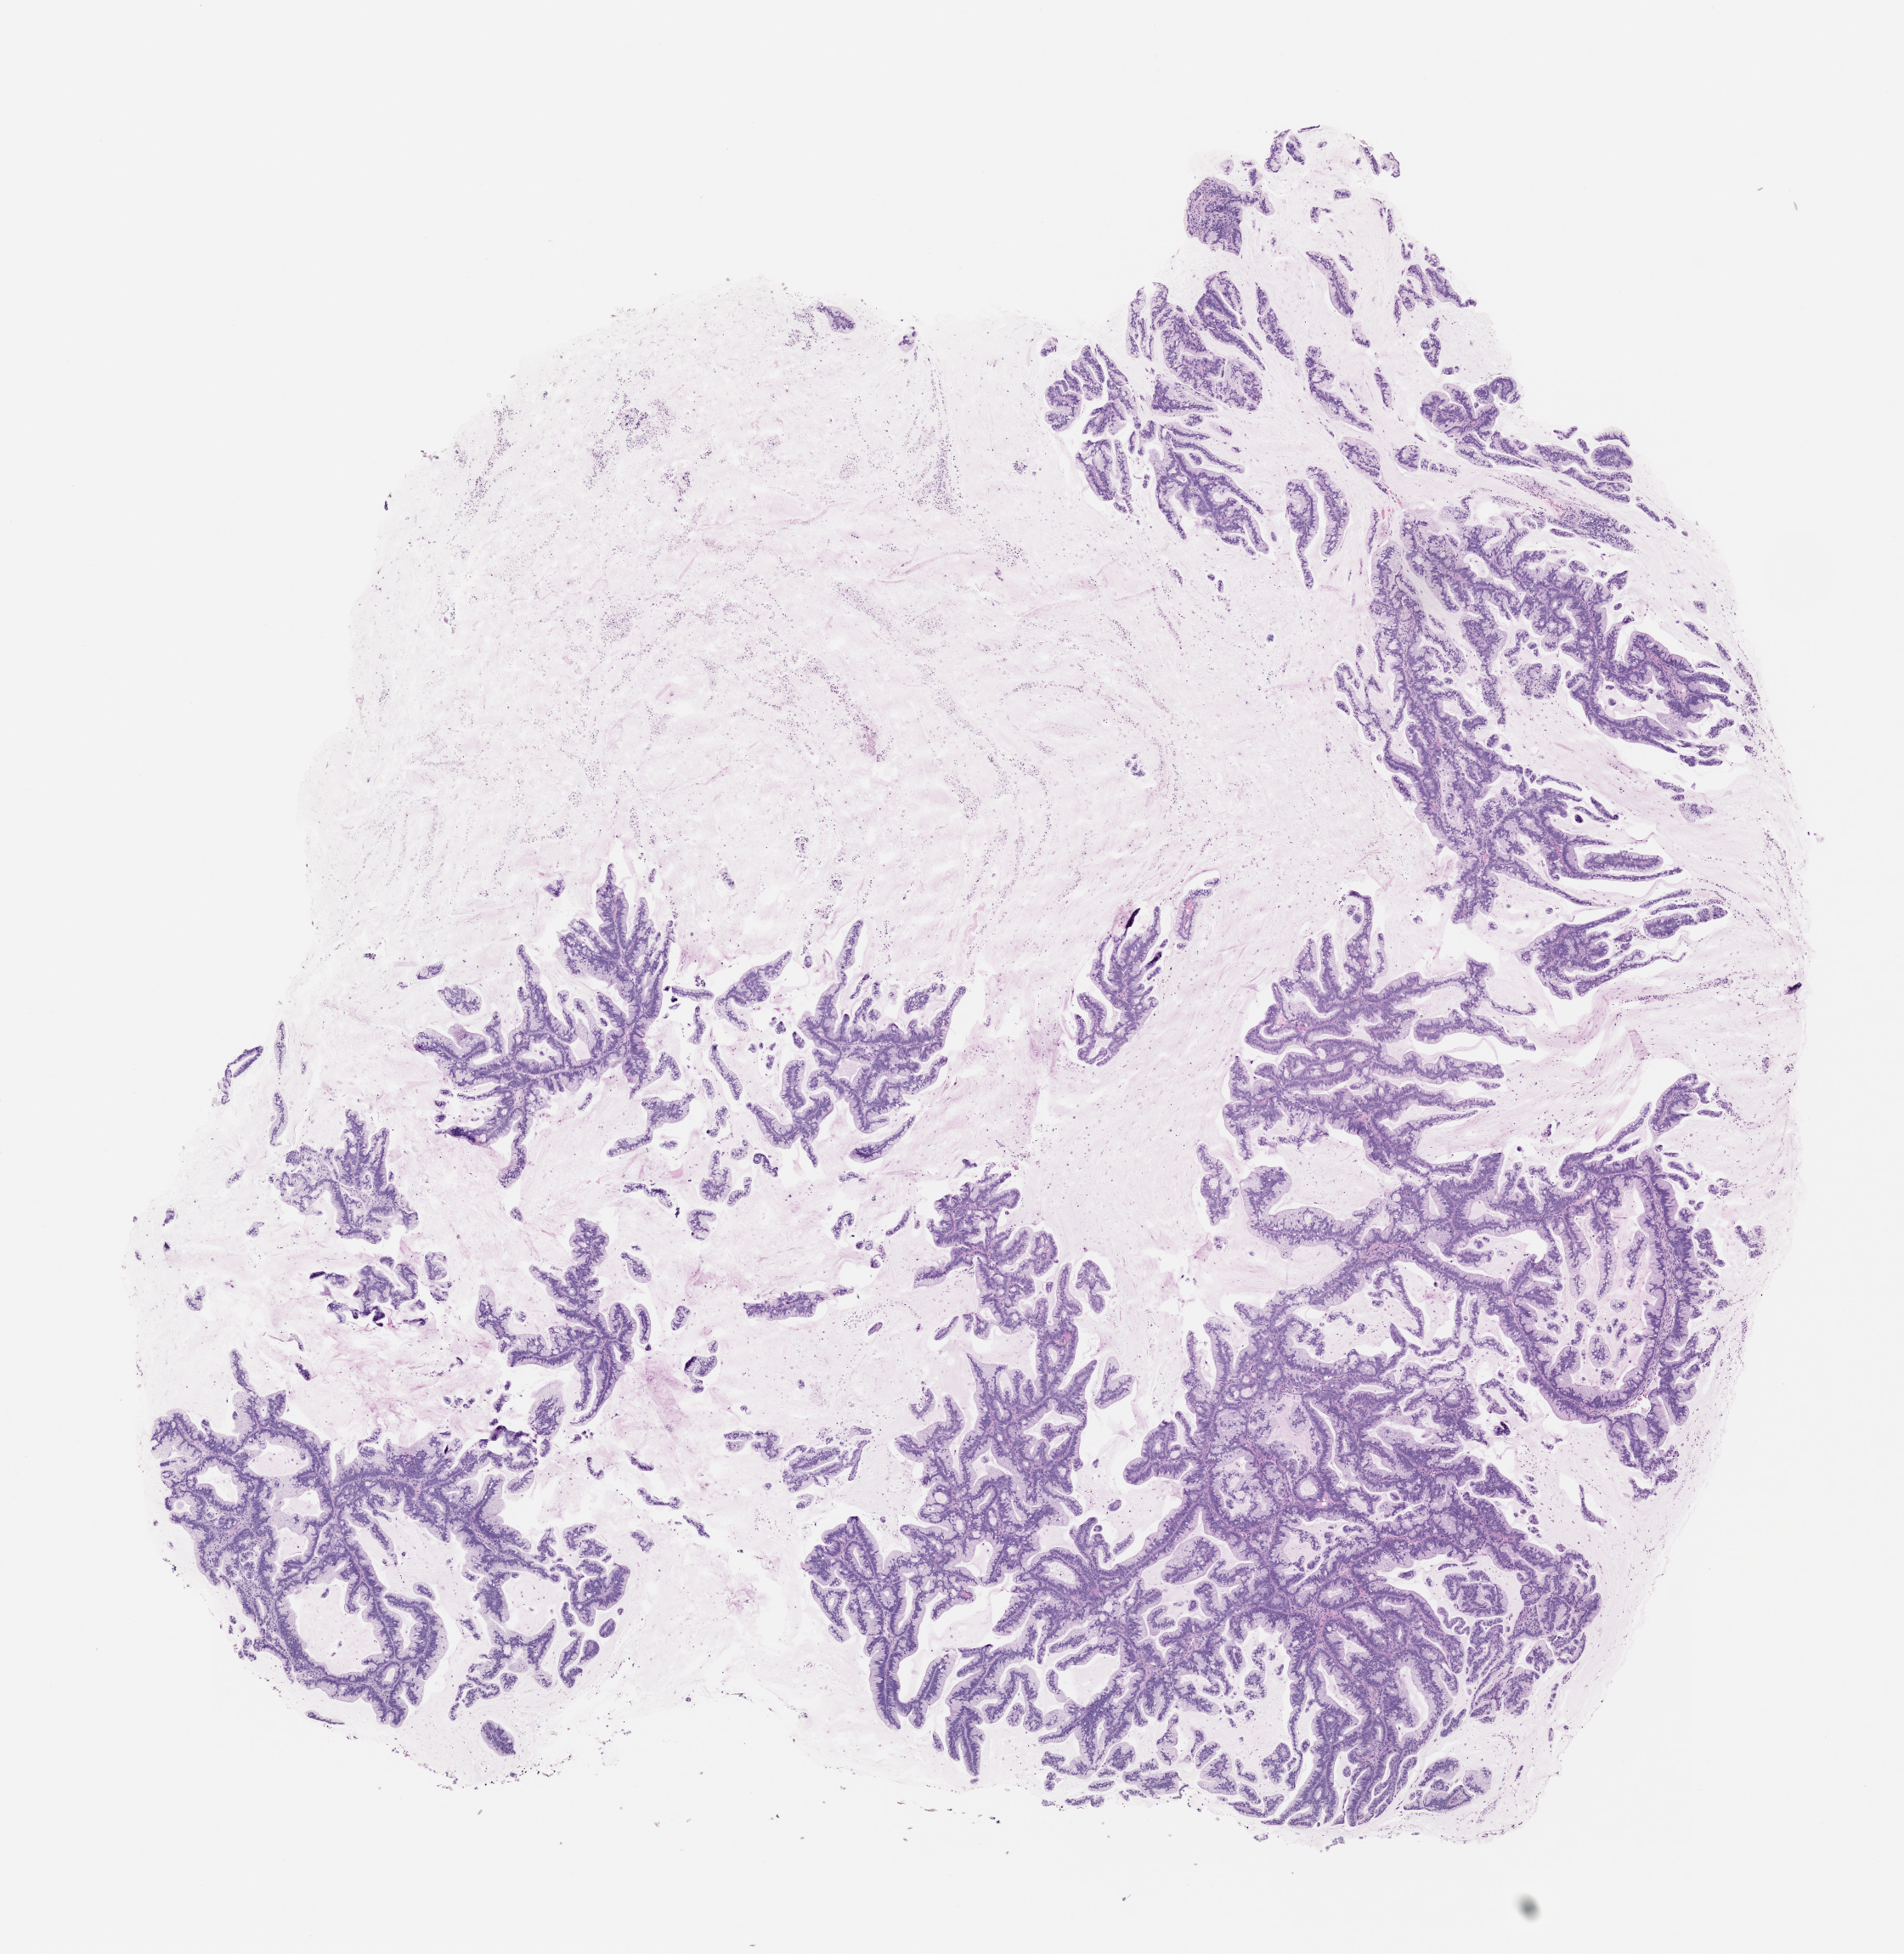
Whole-slide image, H&E: patient-derived xenograft (human tumor grown in a mouse), passage 1 — whole scanned area (about 9.0 x 9.2 mm) shown as a low-resolution overview; formalin-fixed paraffin-embedded section; tumor site category: pancreas.
- originating patient diagnosis: Pancreatic Adenocarcinoma